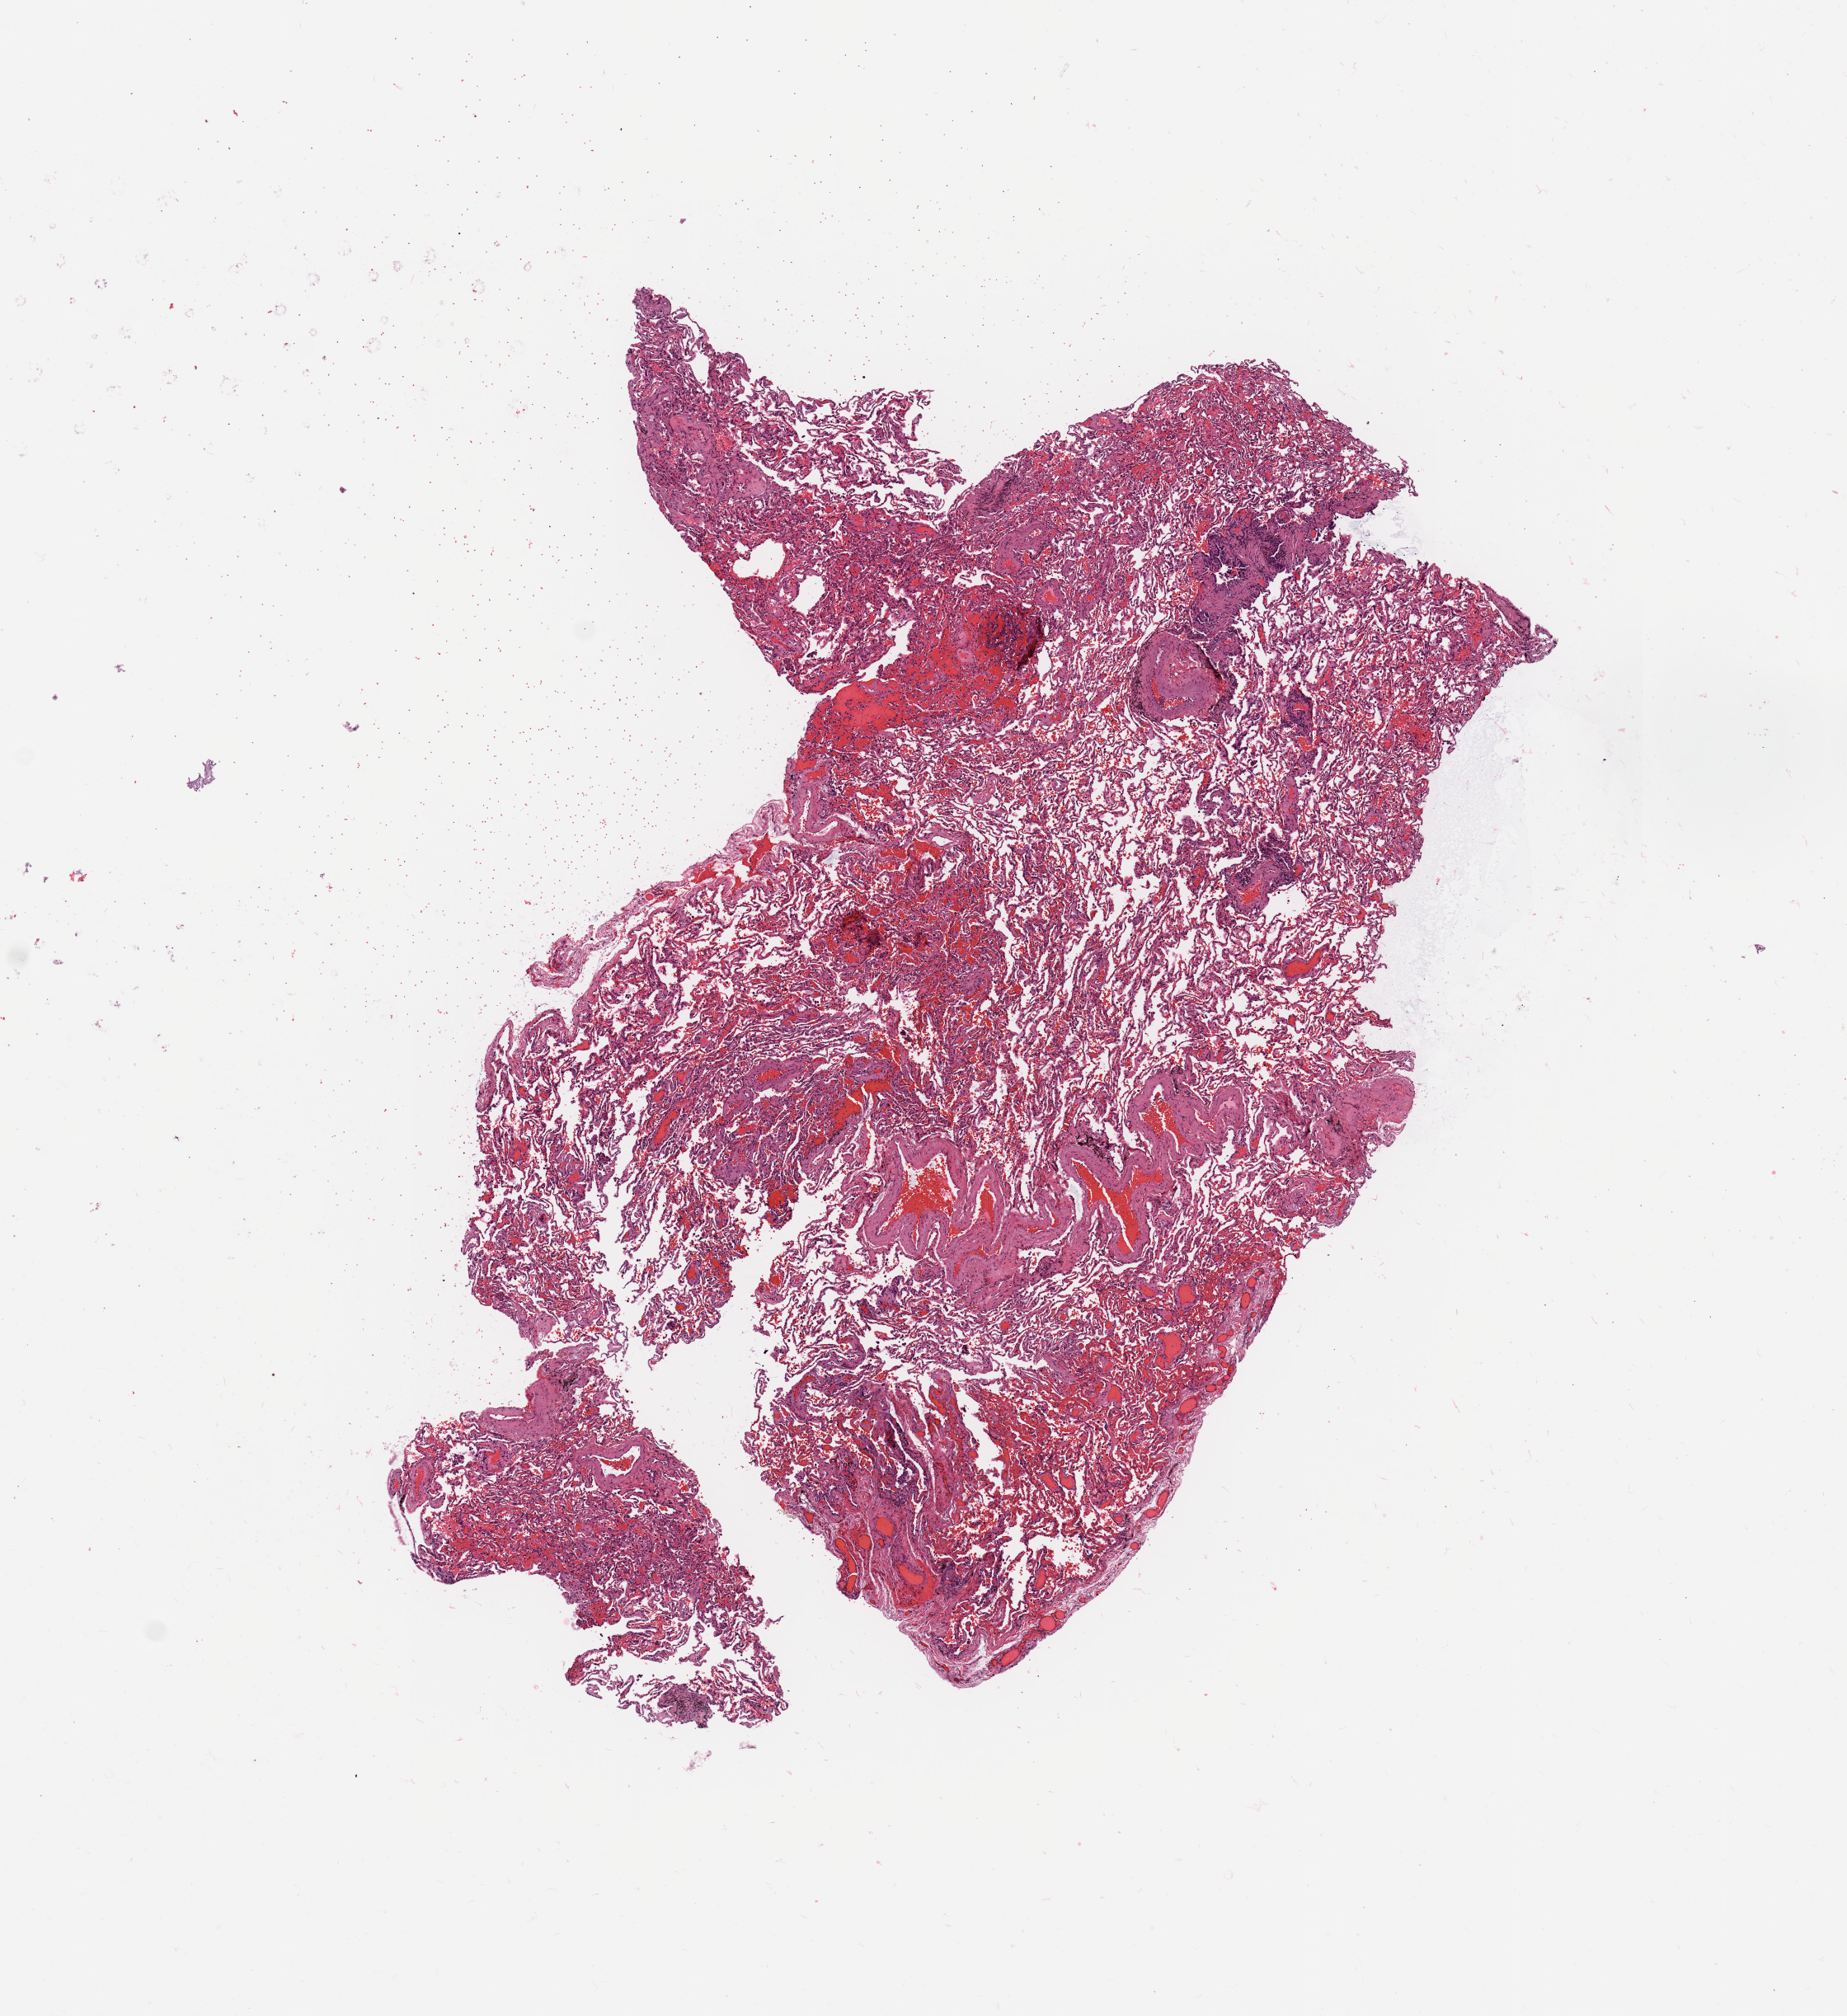
Digitized H&E-stained tissue section (whole slide) — a low-resolution overview of the entire scanned area, about 8.9 x 9.7 mm (slide scanned at 20x), normal (non-tumour) tissue sample, sampled site: lung. 71-year-old male patient.
* this section: normal (non-tumour) tissue from the same patient
* patient diagnosis: Adenocarcinoma, NOS